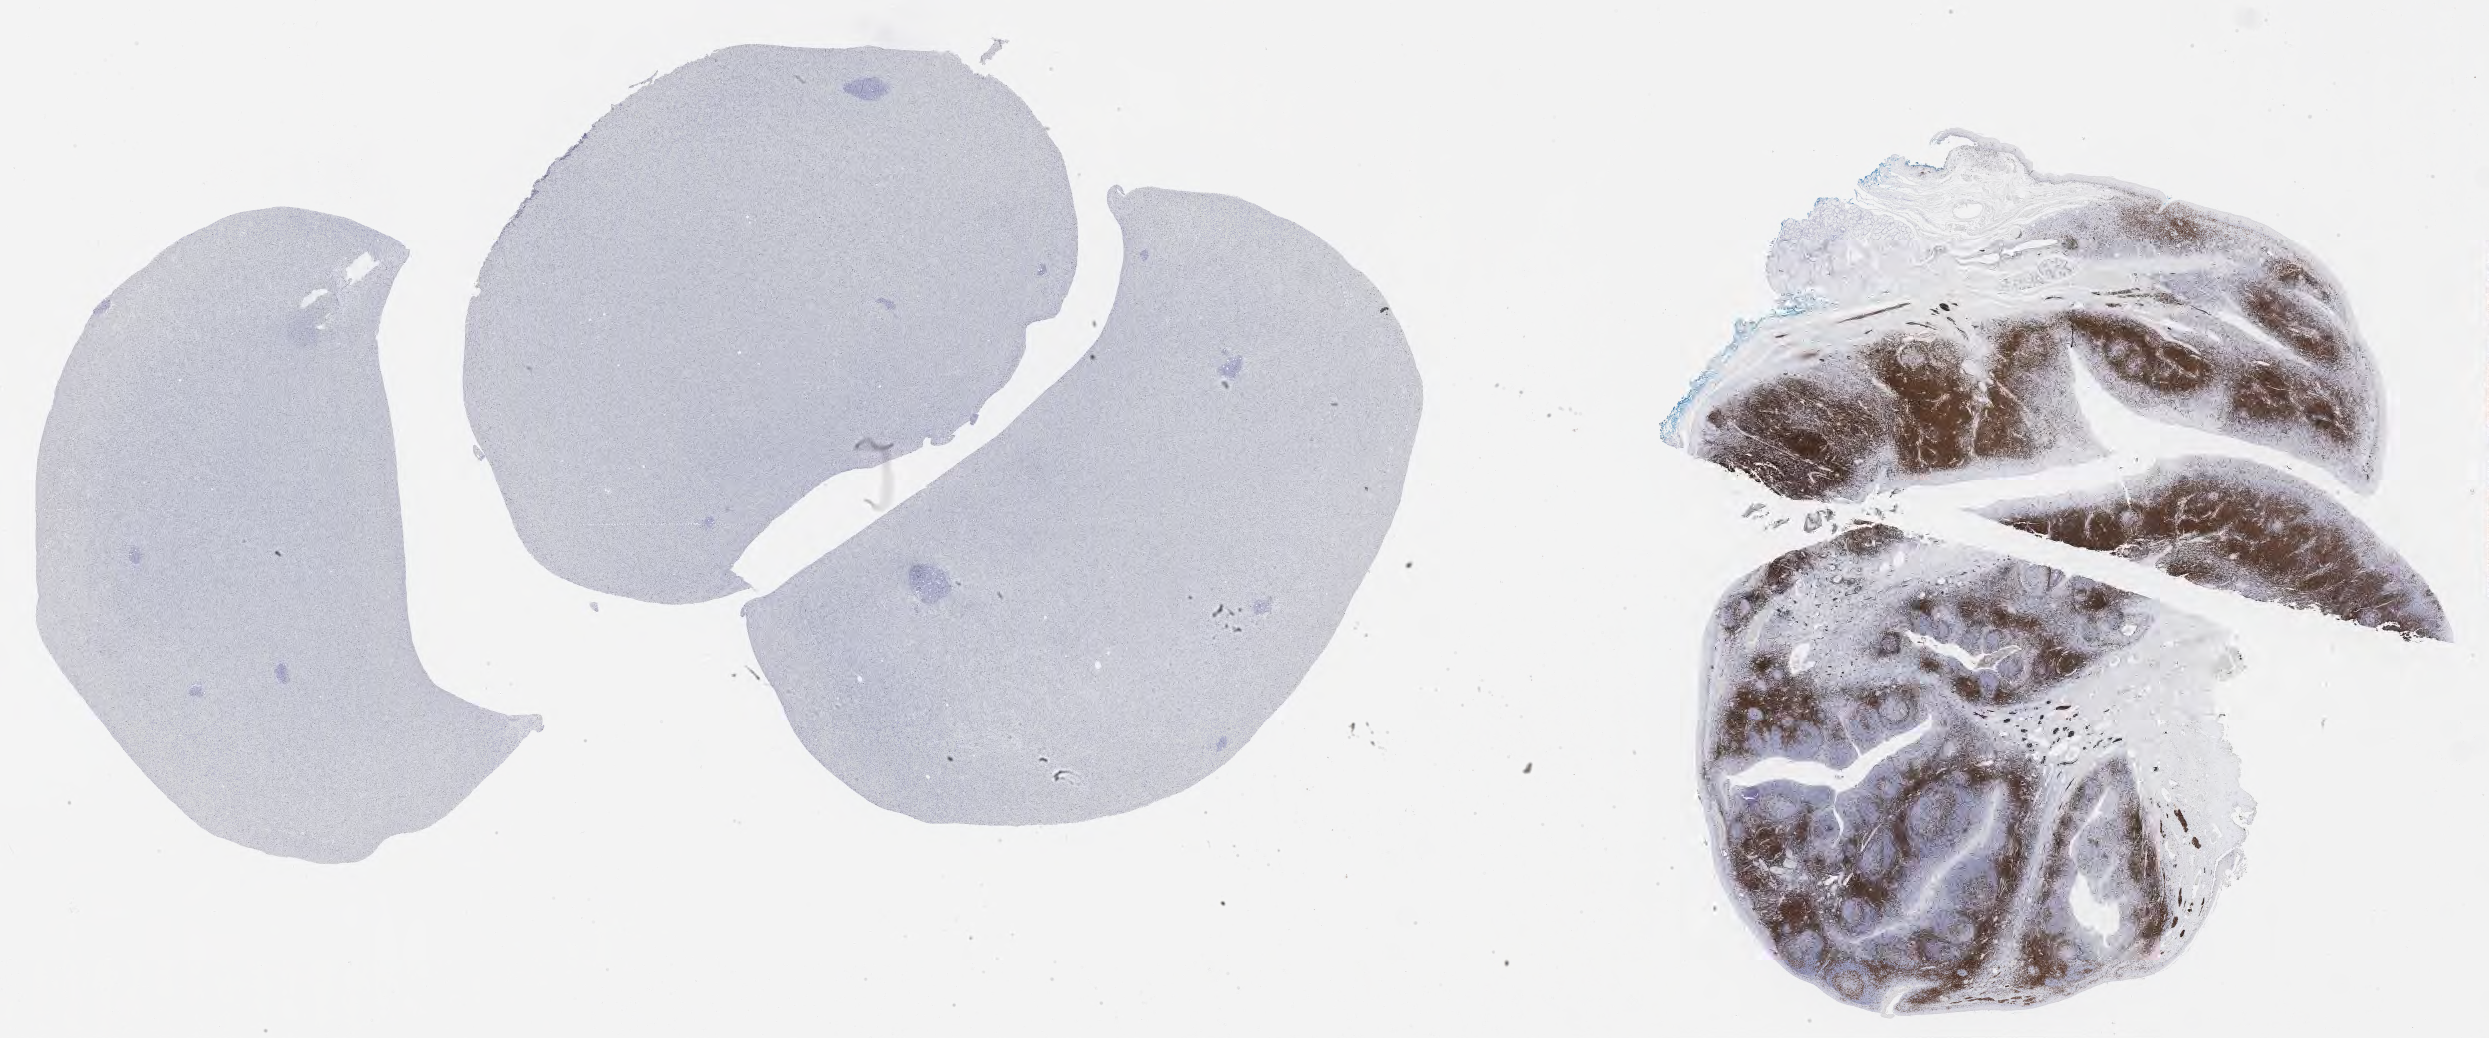
Whole-slide image, immunohistochemical stain for CD3, shown as a low-resolution overview of the whole scanned area (about 40.3 x 16.8 mm), tumor tissue. Patient male; aged 17.
Diagnosis: Burkitt lymphoma, NOS.